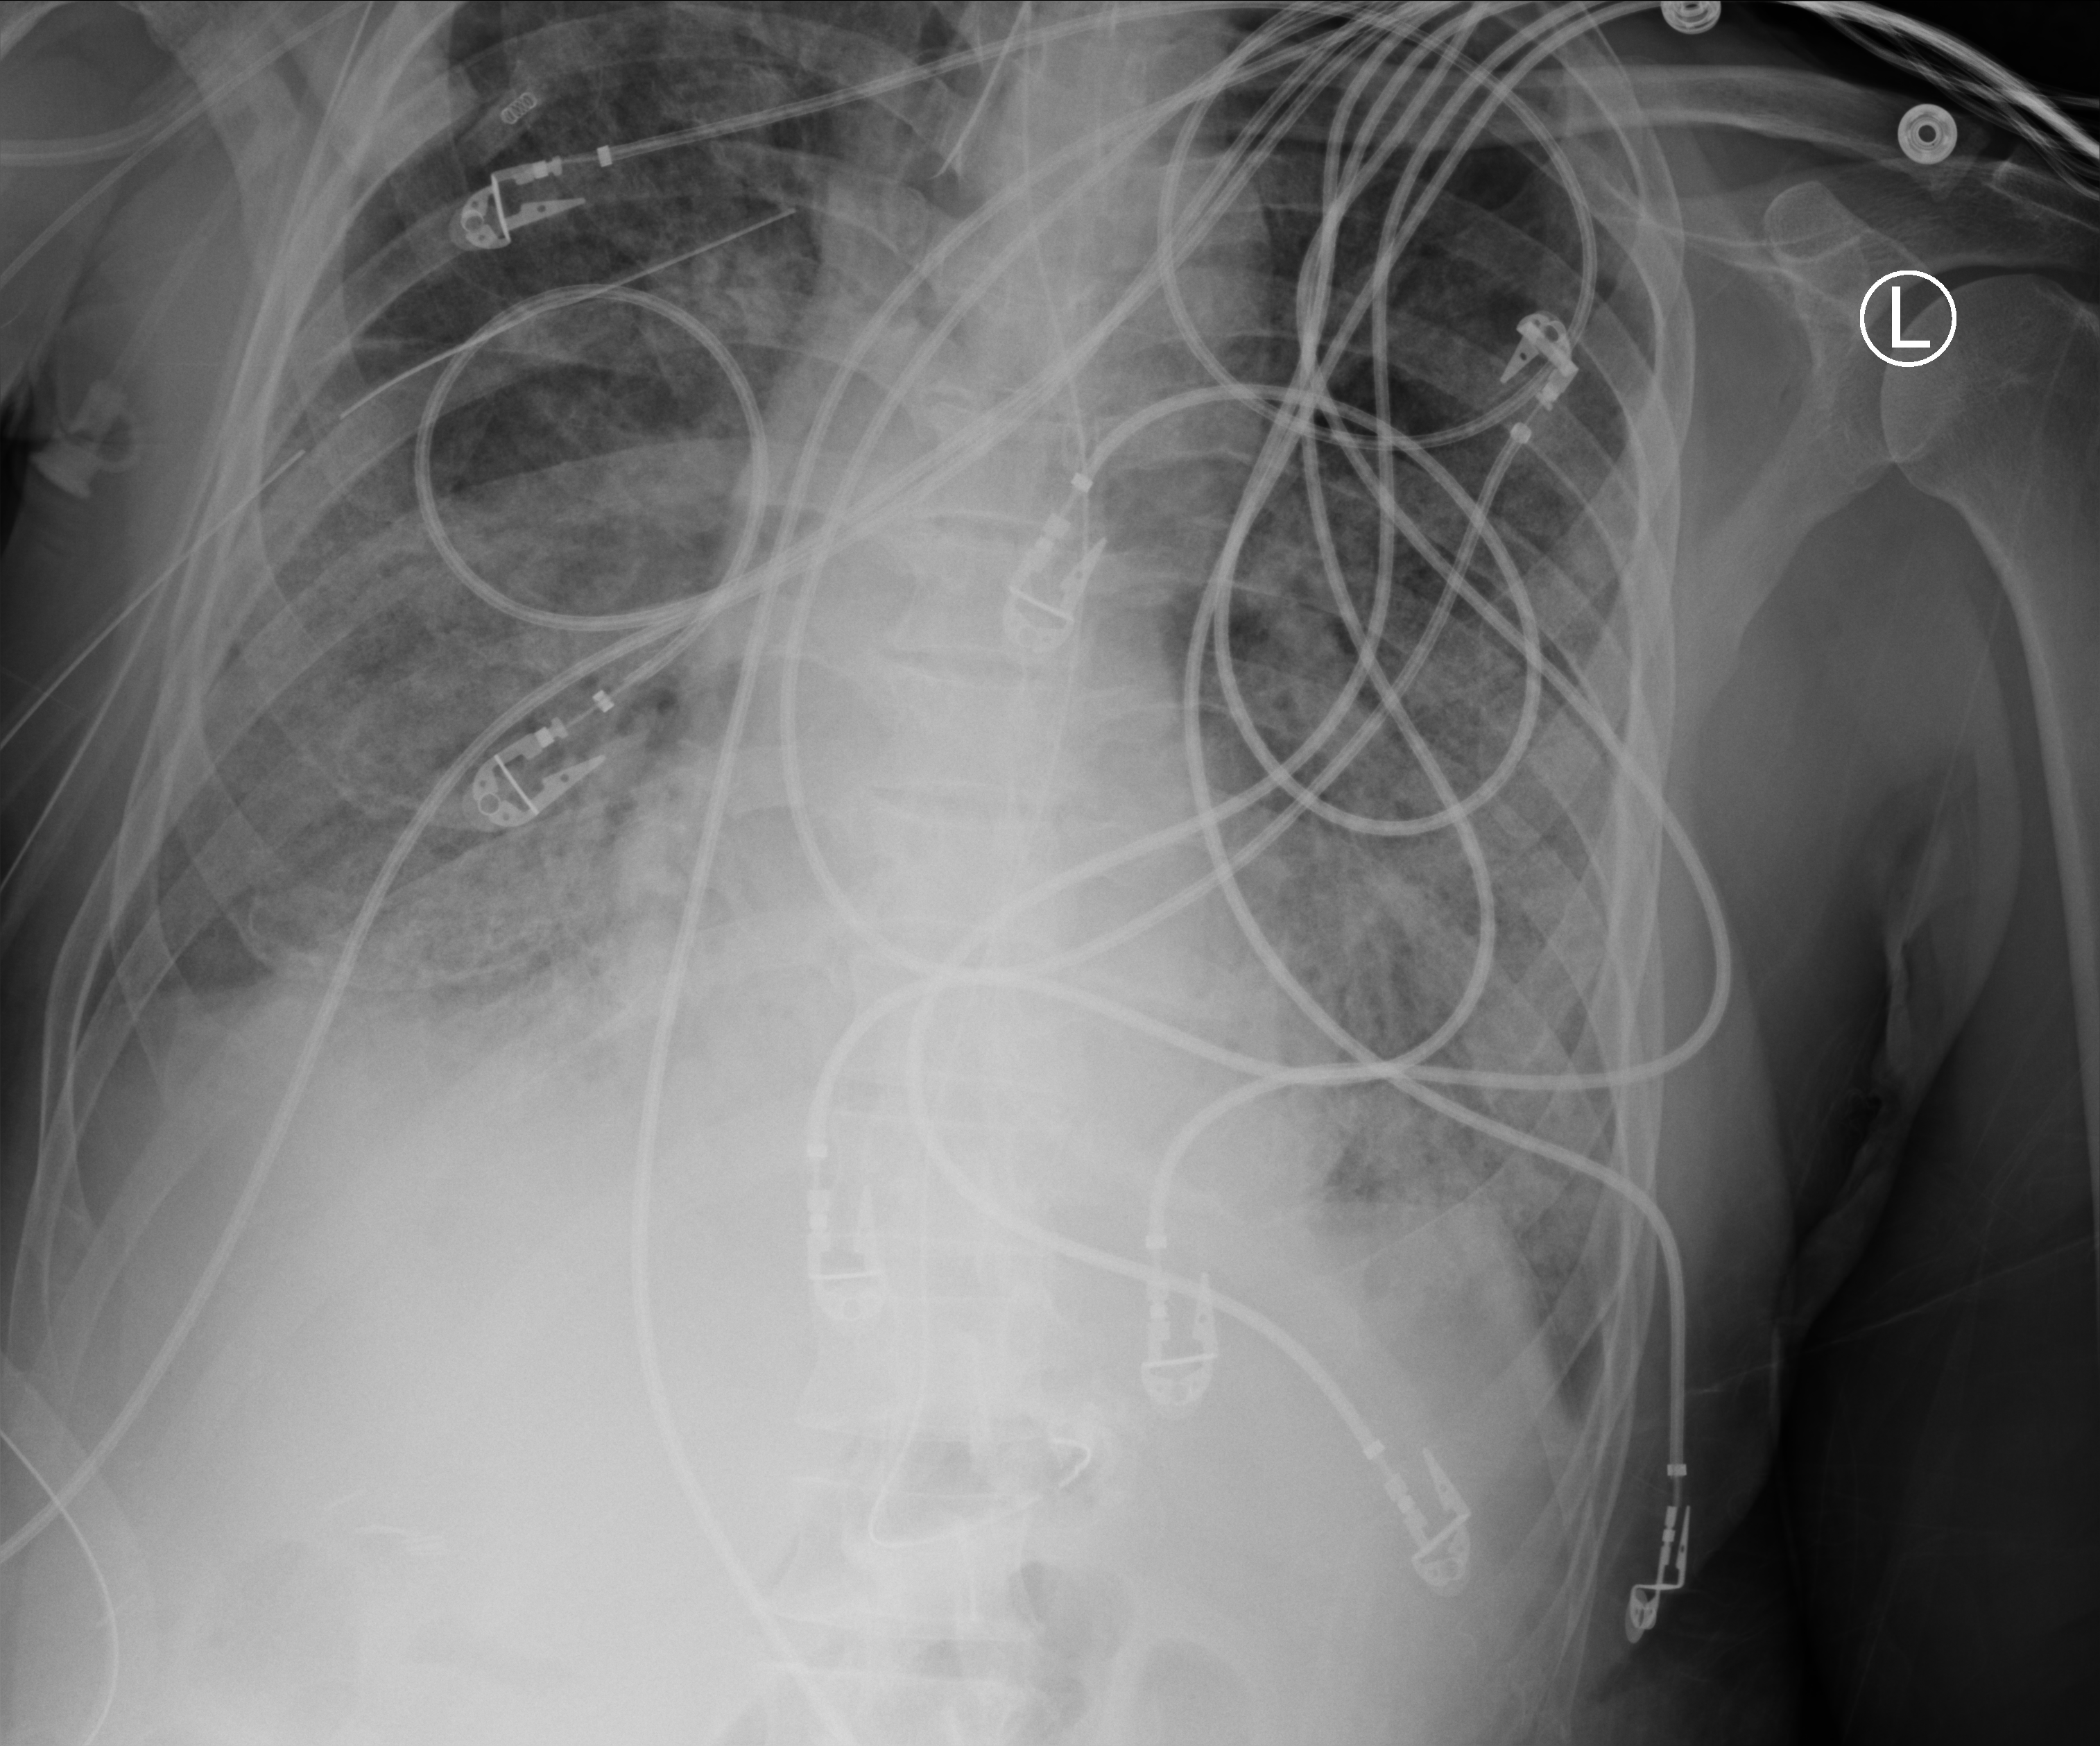
Portable chest radiograph; anteroposterior (AP) projection. Male patient hospitalised with COVID-19, age 60–74 years.
Hospital-stay facts (about this admission, not read from this image; timing relative to this image not recorded): mechanically ventilated during this hospital stay: yes; length of hospital stay: 31 days.